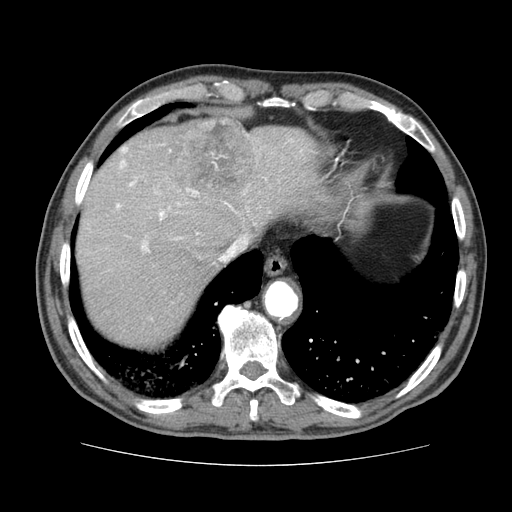
Contrast-enhanced abdominal CT (liver protocol), one axial slice; position 64 of 79 along the scan axis; soft-tissue window (W 400 / L 40 HU); 2.5 mm slice thickness; 512 × 512 image matrix, field of view 360 × 360 mm. Case-level facts recorded for this patient, not image findings: diagnosis: hepatocellular carcinoma (patient treated with transarterial chemoembolisation; whether this scan precedes or follows treatment is not stated here); TNM stage (as recorded): Stage-I; Child-Pugh class: A; tumour nodularity: uninodular.
Outlined on this slice (semi-automatic segmentation, software-assisted and operator-edited):
- liver parenchyma outside the tumour (the mass and vessels are separate outlines, so this box may not span the whole liver): bounding box (x1, y1, x2, y2) in pixels: (76, 118, 329, 344)
- mass: (163, 120, 254, 190)
- liver vessels: (116, 147, 302, 252)